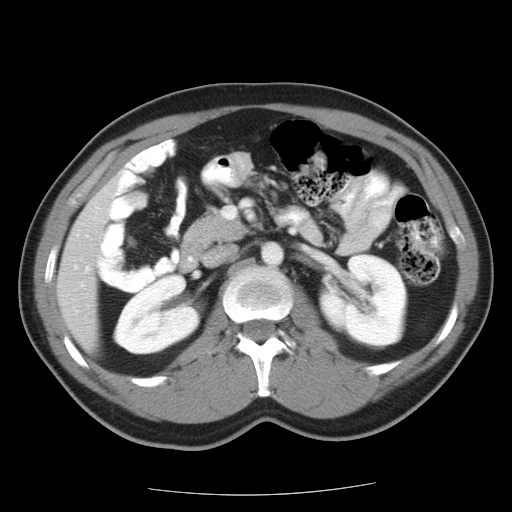
Contrast-enhanced abdominal CT, one axial slice; position 5 of 22 along the scan axis; reconstruction kernel STANDARD; soft-tissue window (W 400 / L 40 HU); 512 × 512 image matrix, field of view 359 × 359 mm. Male patient, age 41 years. Case-level facts recorded for this patient, not image findings: diagnosis: colorectal cancer liver metastases, imaged before liver resection; multiple liver metastases: no; largest metastasis: 2.7 cm.
Annotated regions visible in this slice (outlined manually by an expert reader):
- liver: bounding box <58,192,108,343> (left, top, right, bottom; pixels)
- planned liver remnant (the part of the liver to remain after resection): <59,191,109,343>